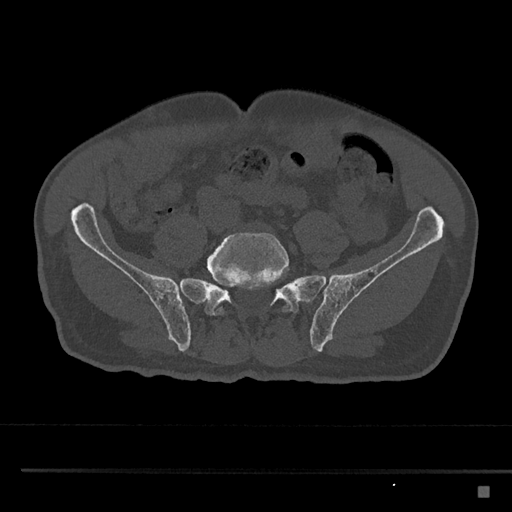
CT including the spine, one axial slice. Slice 559 of 797 in the series (ordered by position). 120 kVp. Bone window (W 1800 / L 400 HU). 512 × 512 image matrix, field of view 391 × 391 mm. Male patient, age 59 years. Case-level facts recorded for this patient, not image findings: primary cancer: prostate.
Annotated regions visible in this slice (semi-automatic segmentation, software-assisted and operator-edited):
- L5 vertebra: bounding box <207,232,291,316> (left, top, right, bottom; pixels)